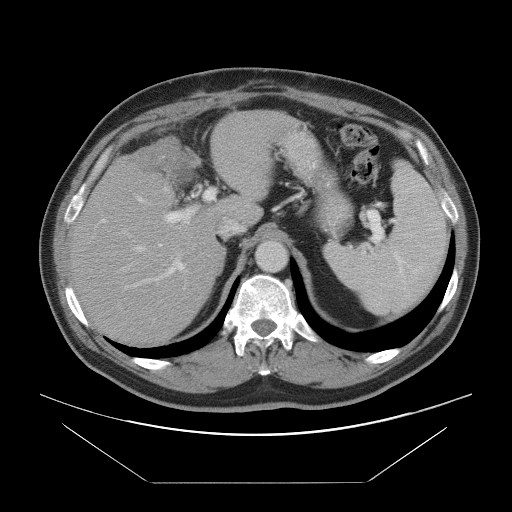
Contrast-enhanced abdominal CT, one axial slice. Position 62 of 97 along the scan axis. Intravenous contrast given. Soft-tissue window (W 400 / L 40 HU). 5 mm slice thickness. 512 × 512 image matrix. Male patient, age 62 years. From the clinical record (not read from this slice): diagnosis: colorectal cancer liver metastases, imaged before liver resection; multiple liver metastases: no; largest metastasis: 7 cm.
Outlined on this slice (outlined manually by an expert reader):
- hepatic veins: bounding box (x1, y1, x2, y2) in pixels: (118, 186, 246, 270)
- liver: (72, 112, 292, 345)
- planned liver remnant (the part of the liver to remain after resection): (72, 173, 231, 345)
- portal vein (with intrahepatic branches): (100, 189, 216, 289)
- liver metastasis: (131, 144, 187, 173)